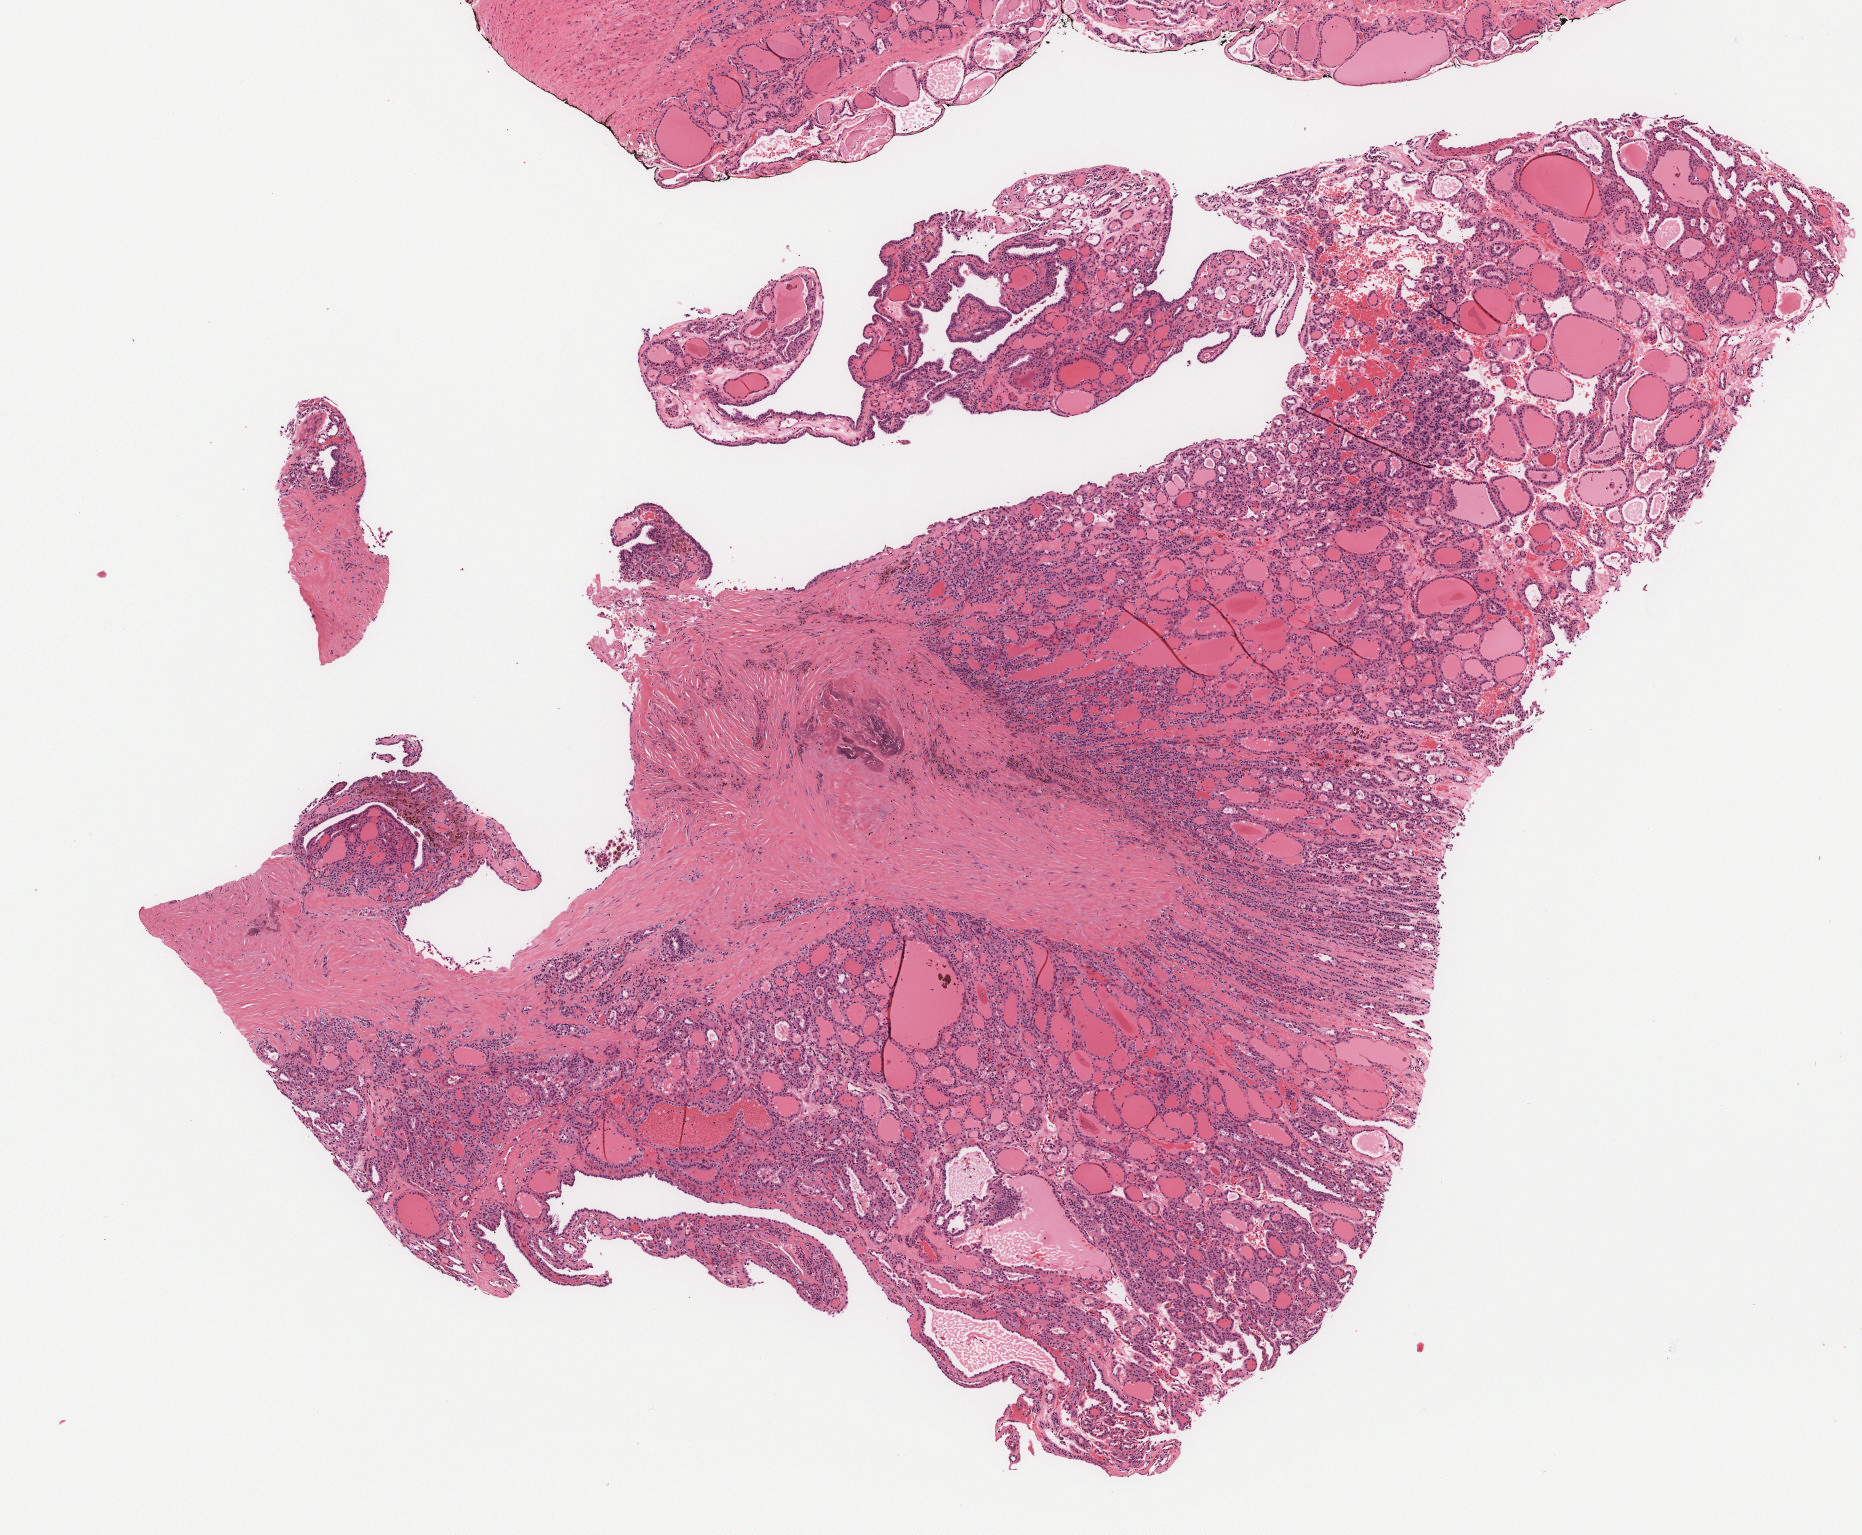
Whole-slide histology image, H&E-stained, whole scanned area (about 7.5 x 6.2 mm, acquisition: 40x scan) shown as a low-resolution overview; formalin-fixed paraffin-embedded (FFPE) diagnostic section; thyroid, primary tumour sample. Female, age 31 years at initial diagnosis.
* TNM: T2 NX MX
* AJCC pathologic stage: I (7th edition)
* pathologic diagnosis: Papillary carcinoma, follicular variant (thyroid gland)